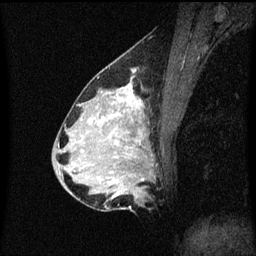
Breast MRI (dynamic contrast-enhanced), one sagittal slice. Slice 27 of 60 in the series (ordered by position). Dynamic contrast-enhanced series, image 2 of 3 at this slice position (ordered by acquisition). 1.5 T. TE 4.2 ms, TR 8.4 ms. 256 × 256 image matrix, field of view 200 × 200 mm. Patient: female, 34 years. Case-level facts recorded for this patient, not image findings: setting: breast cancer imaged before/during neoadjuvant chemotherapy; receptor status: HR-positive, HER2-negative.
Outlined on this slice (semi-automatic segmentation, software-assisted and operator-edited):
- analysis volume of interest (the breast-tissue region the enhancement analysis was run in; not a lesion): box from (x=69, y=70) to (x=156, y=209) px
- tumour enhancement mask (voxels above the 70 % enhancement threshold inside the analysis volume of interest): (x=109, y=84)–(x=143, y=149)